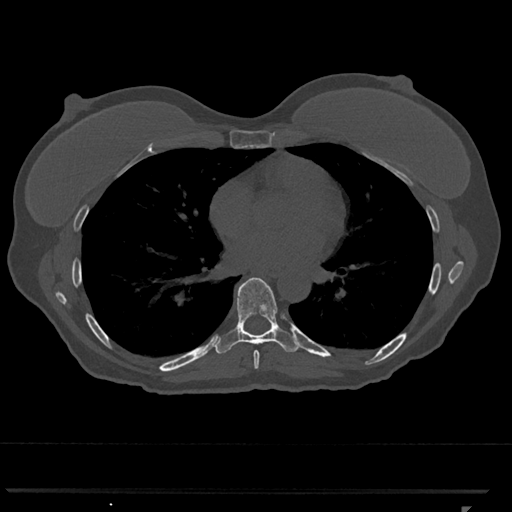
CT including the spine, one axial slice; position 673 of 793 along the scan axis; reconstruction kernel Br40s/3; bone window (W 1800 / L 400 HU); 512 × 512 image matrix, field of view 380 × 380 mm. Patient: female, 62 years. From the clinical record (not read from this slice): primary cancer: renal.
Outlined on this slice (semi-automatically segmented with operator editing):
- T7 vertebra: bounding box (x1, y1, x2, y2) in pixels: (253, 351, 260, 369)
- T8 vertebra: (214, 277, 299, 354)